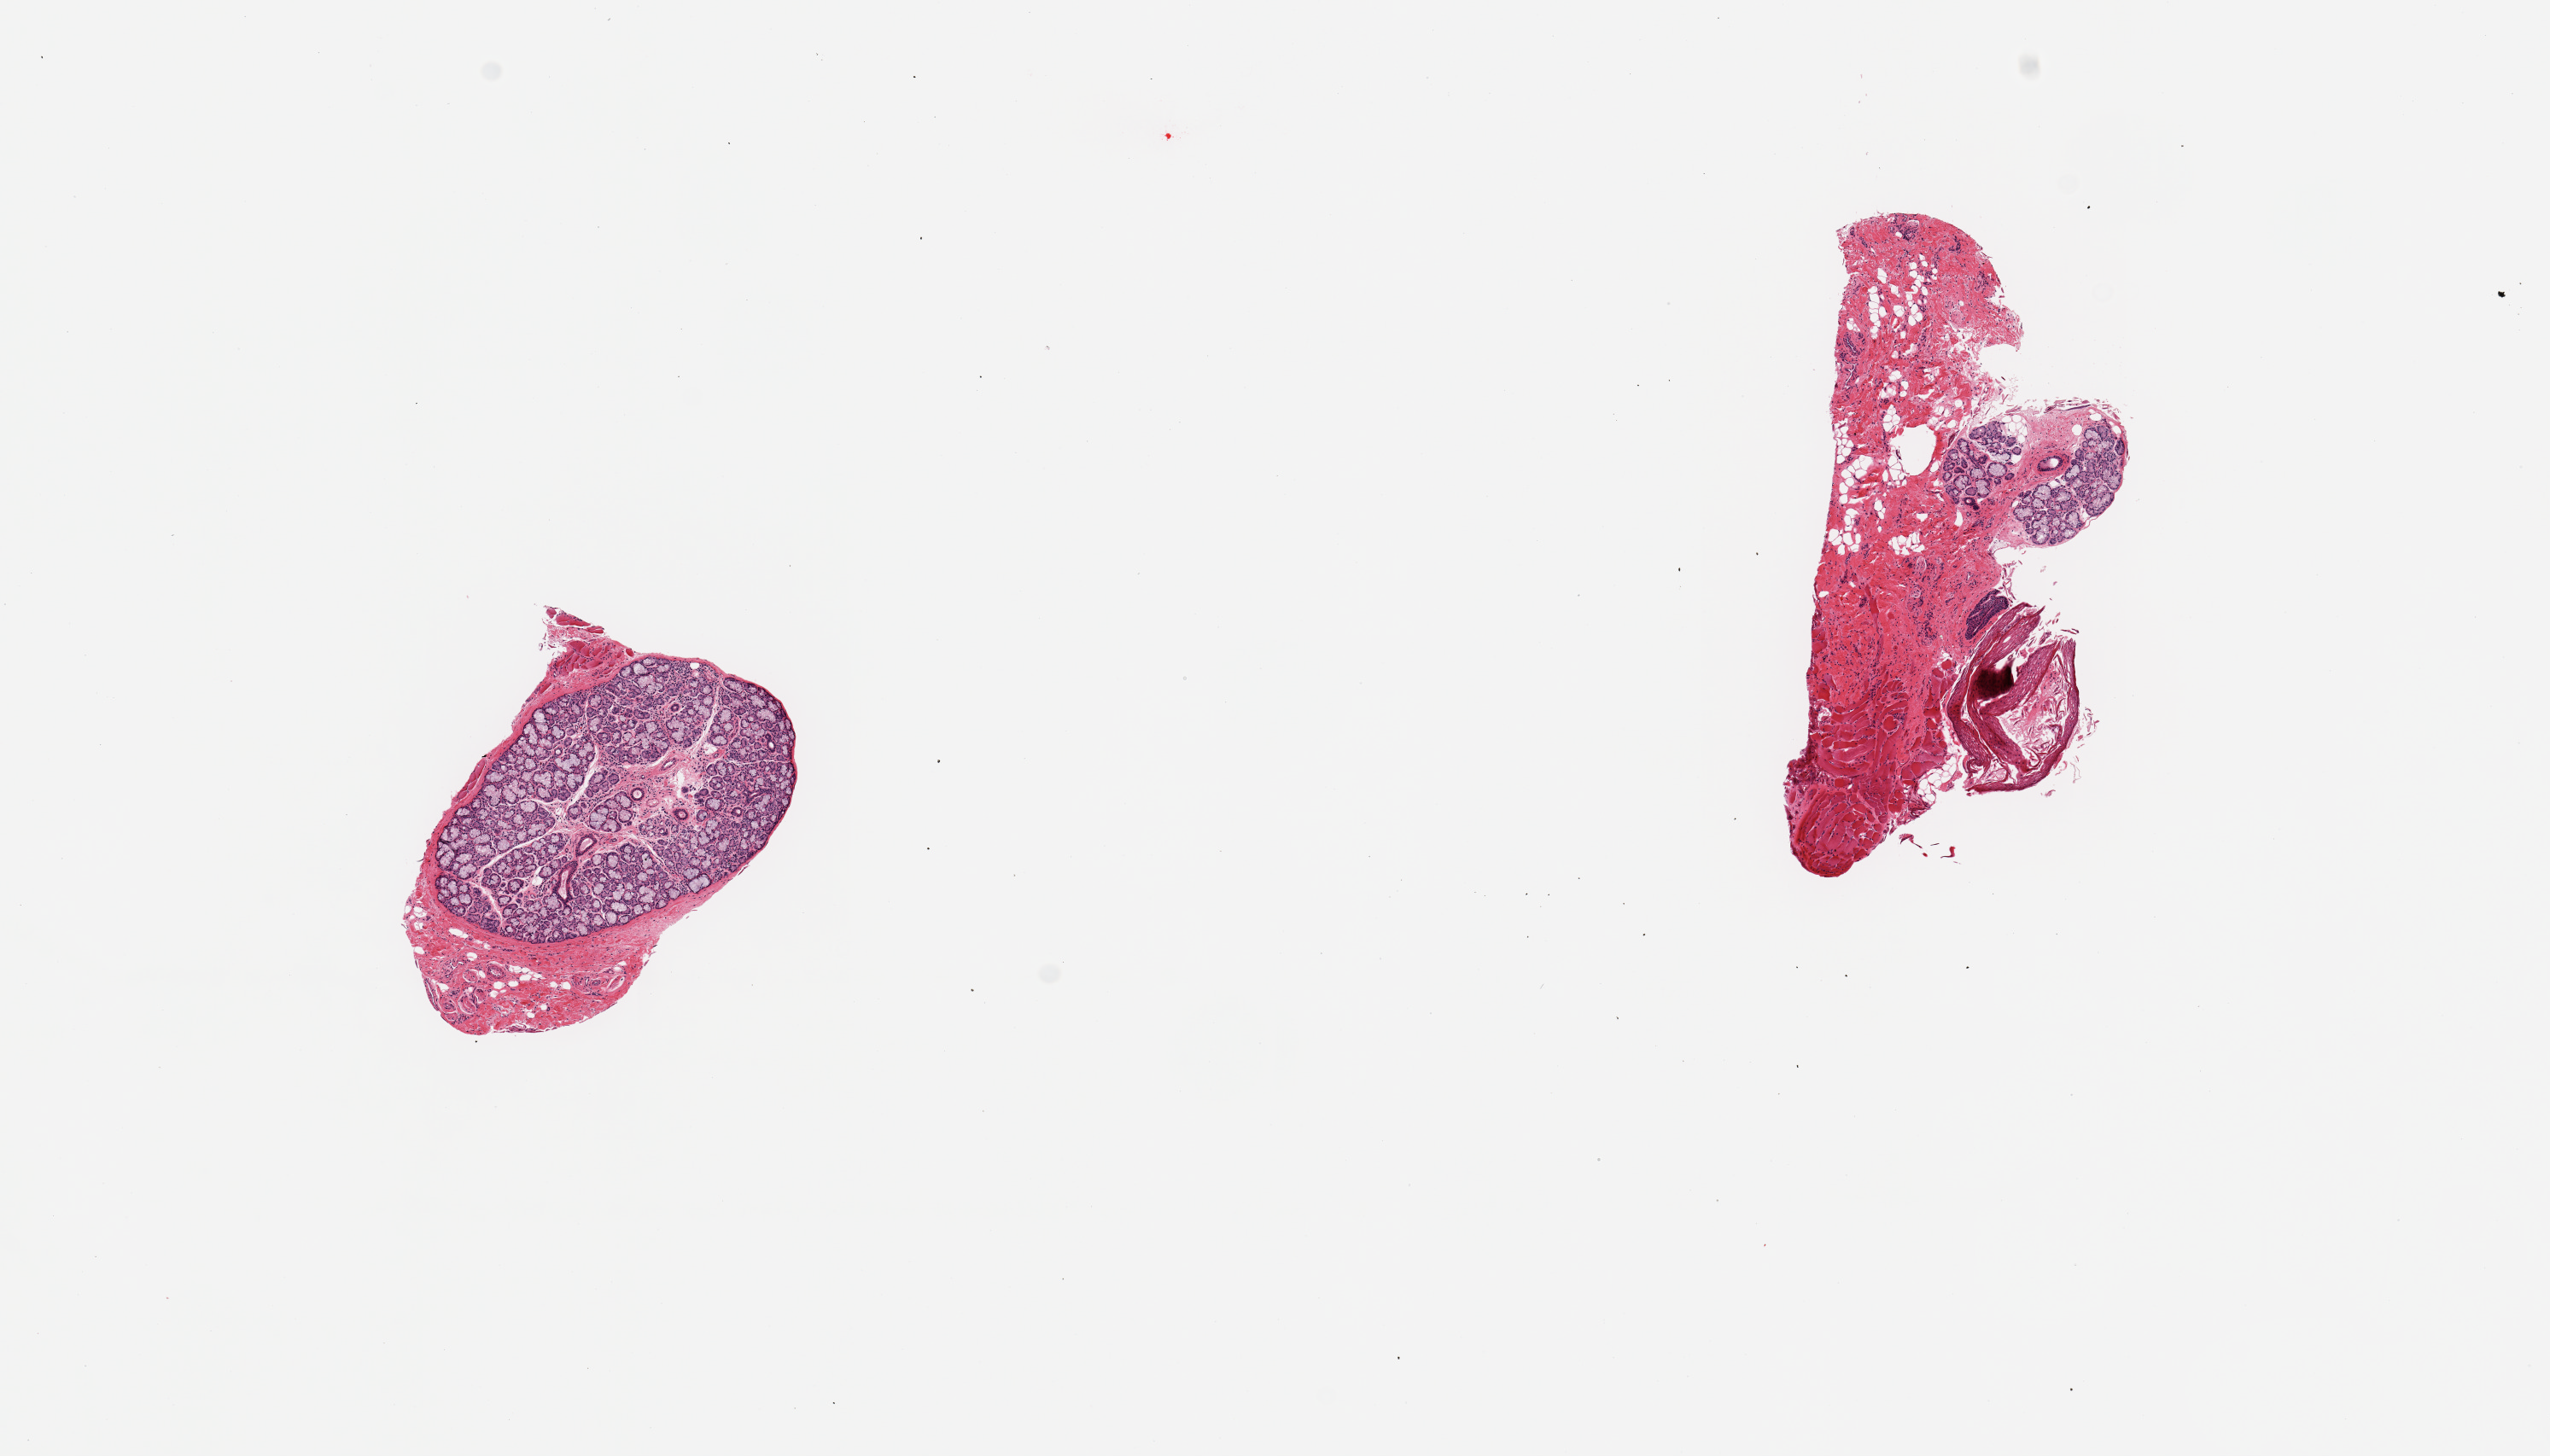
Haematoxylin and eosin whole-slide image, brightfield — low-resolution overview of the scanned area, about 11.8 x 6.7 mm; PAXgene-fixed paraffin-embedded (PFPE) section; target tissue: minor salivary gland; tissue donor sample.
Reviewer comment on this tissue sample: 2 pieces; salivary gland elements with mild chronic inflammation, 1 piece is ~80% salivary gland with 20% stroma/skeletal muscle, 2nd is only ~10% gland with stroma, lip, skeletal muscle.